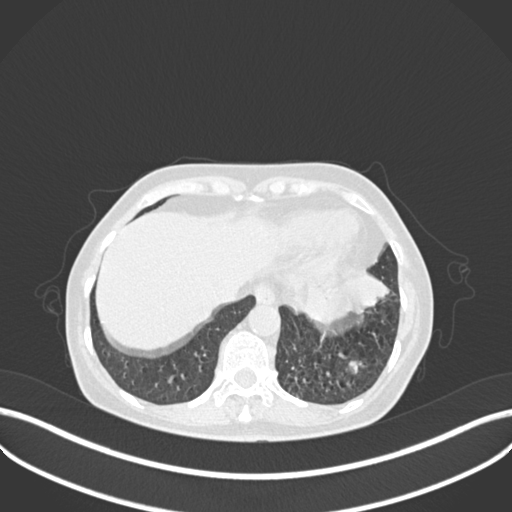
Chest CT, one axial slice; position 50 of 270 along the scan axis; reconstruction kernel B30f; lung window (W 1500 / L -600 HU); 1 mm slice thickness; 512 × 512 image matrix, field of view 400 × 400 mm. Patient: female, 63 years. Case-level facts recorded for this patient, not image findings: clinical TNM (as recorded): T1b N0 M0.
Structures marked on this image (bounding box drawn by a radiologist):
- lung tumour (recorded histology: adenocarcinoma): bounding box (x1, y1, x2, y2) in pixels: (302, 256, 389, 340)